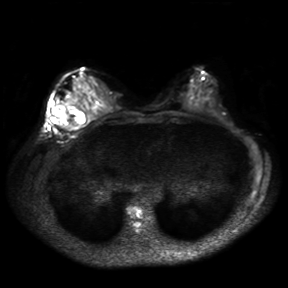
Breast MRI, one axial slice. Slice 15 of 30 in the series (ordered by position). Diffusion-weighted series; image 2 of 4 stored at this slice position (different b-values; order by instance number). 3 T. 288 × 288 image matrix. Female patient.
Outlined on this slice (manually delineated by an expert):
- tumour on diffusion-weighted imaging: bounding box (x1, y1, x2, y2) in pixels: (52, 104, 71, 130)